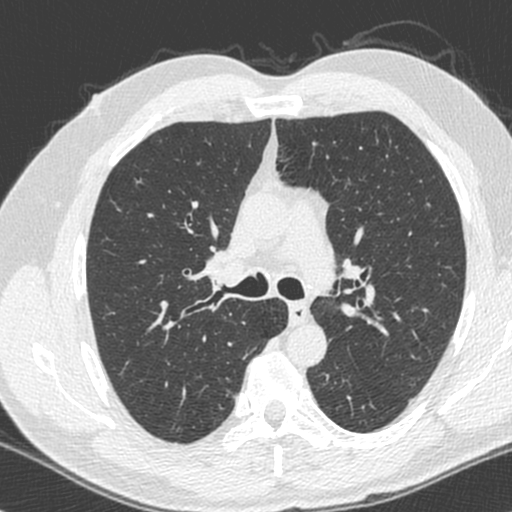
Low-dose screening chest CT, axial slice. Baseline screening round. Lung window (W 1500 / L -600 HU). 1.3 mm slice thickness. 512 × 512 image matrix, field of view 319 × 319 mm. Male, age 55 years at enrolment.
• Lesion marked by an expert reader, bounding box <219,380,249,408> (left, top, right, bottom; pixels).
• Screening reader's record for this exam: no non-calcified nodule ≥4 mm recorded.
• Official screen result: negative screen, minor abnormalities not suspicious for lung cancer.
• Lung cancer was diagnosed 1039 days after this screen: adenocarcinoma, NOS, right upper lobe, poorly differentiated (G3), stage IA (AJCC 6th edition), 15 mm at pathology.